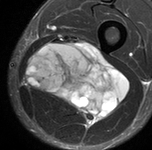
MRI of an extremity soft-tissue mass, one axial slice. Position 43 of 90 along the scan axis. STIR. MR volume resampled by the dataset authors to the PET/CT grid (not the native acquisition matrix). 3.27 mm slice thickness. 152 × 150 image matrix, field of view 148 × 146 mm. Male patient. From the clinical record (not read from this slice): histological type: undifferentiated pleomorphic liposarcoma; grade: high; site of the primary tumour: left thigh.
Structures marked on this image (expert contour drawn on MRI and transferred to this co-registered scan by the dataset authors):
- gross tumour volume including surrounding oedema: bounding box <25,43,129,124> (left, top, right, bottom; pixels)
- gross tumour volume (mass): <25,43,129,124>